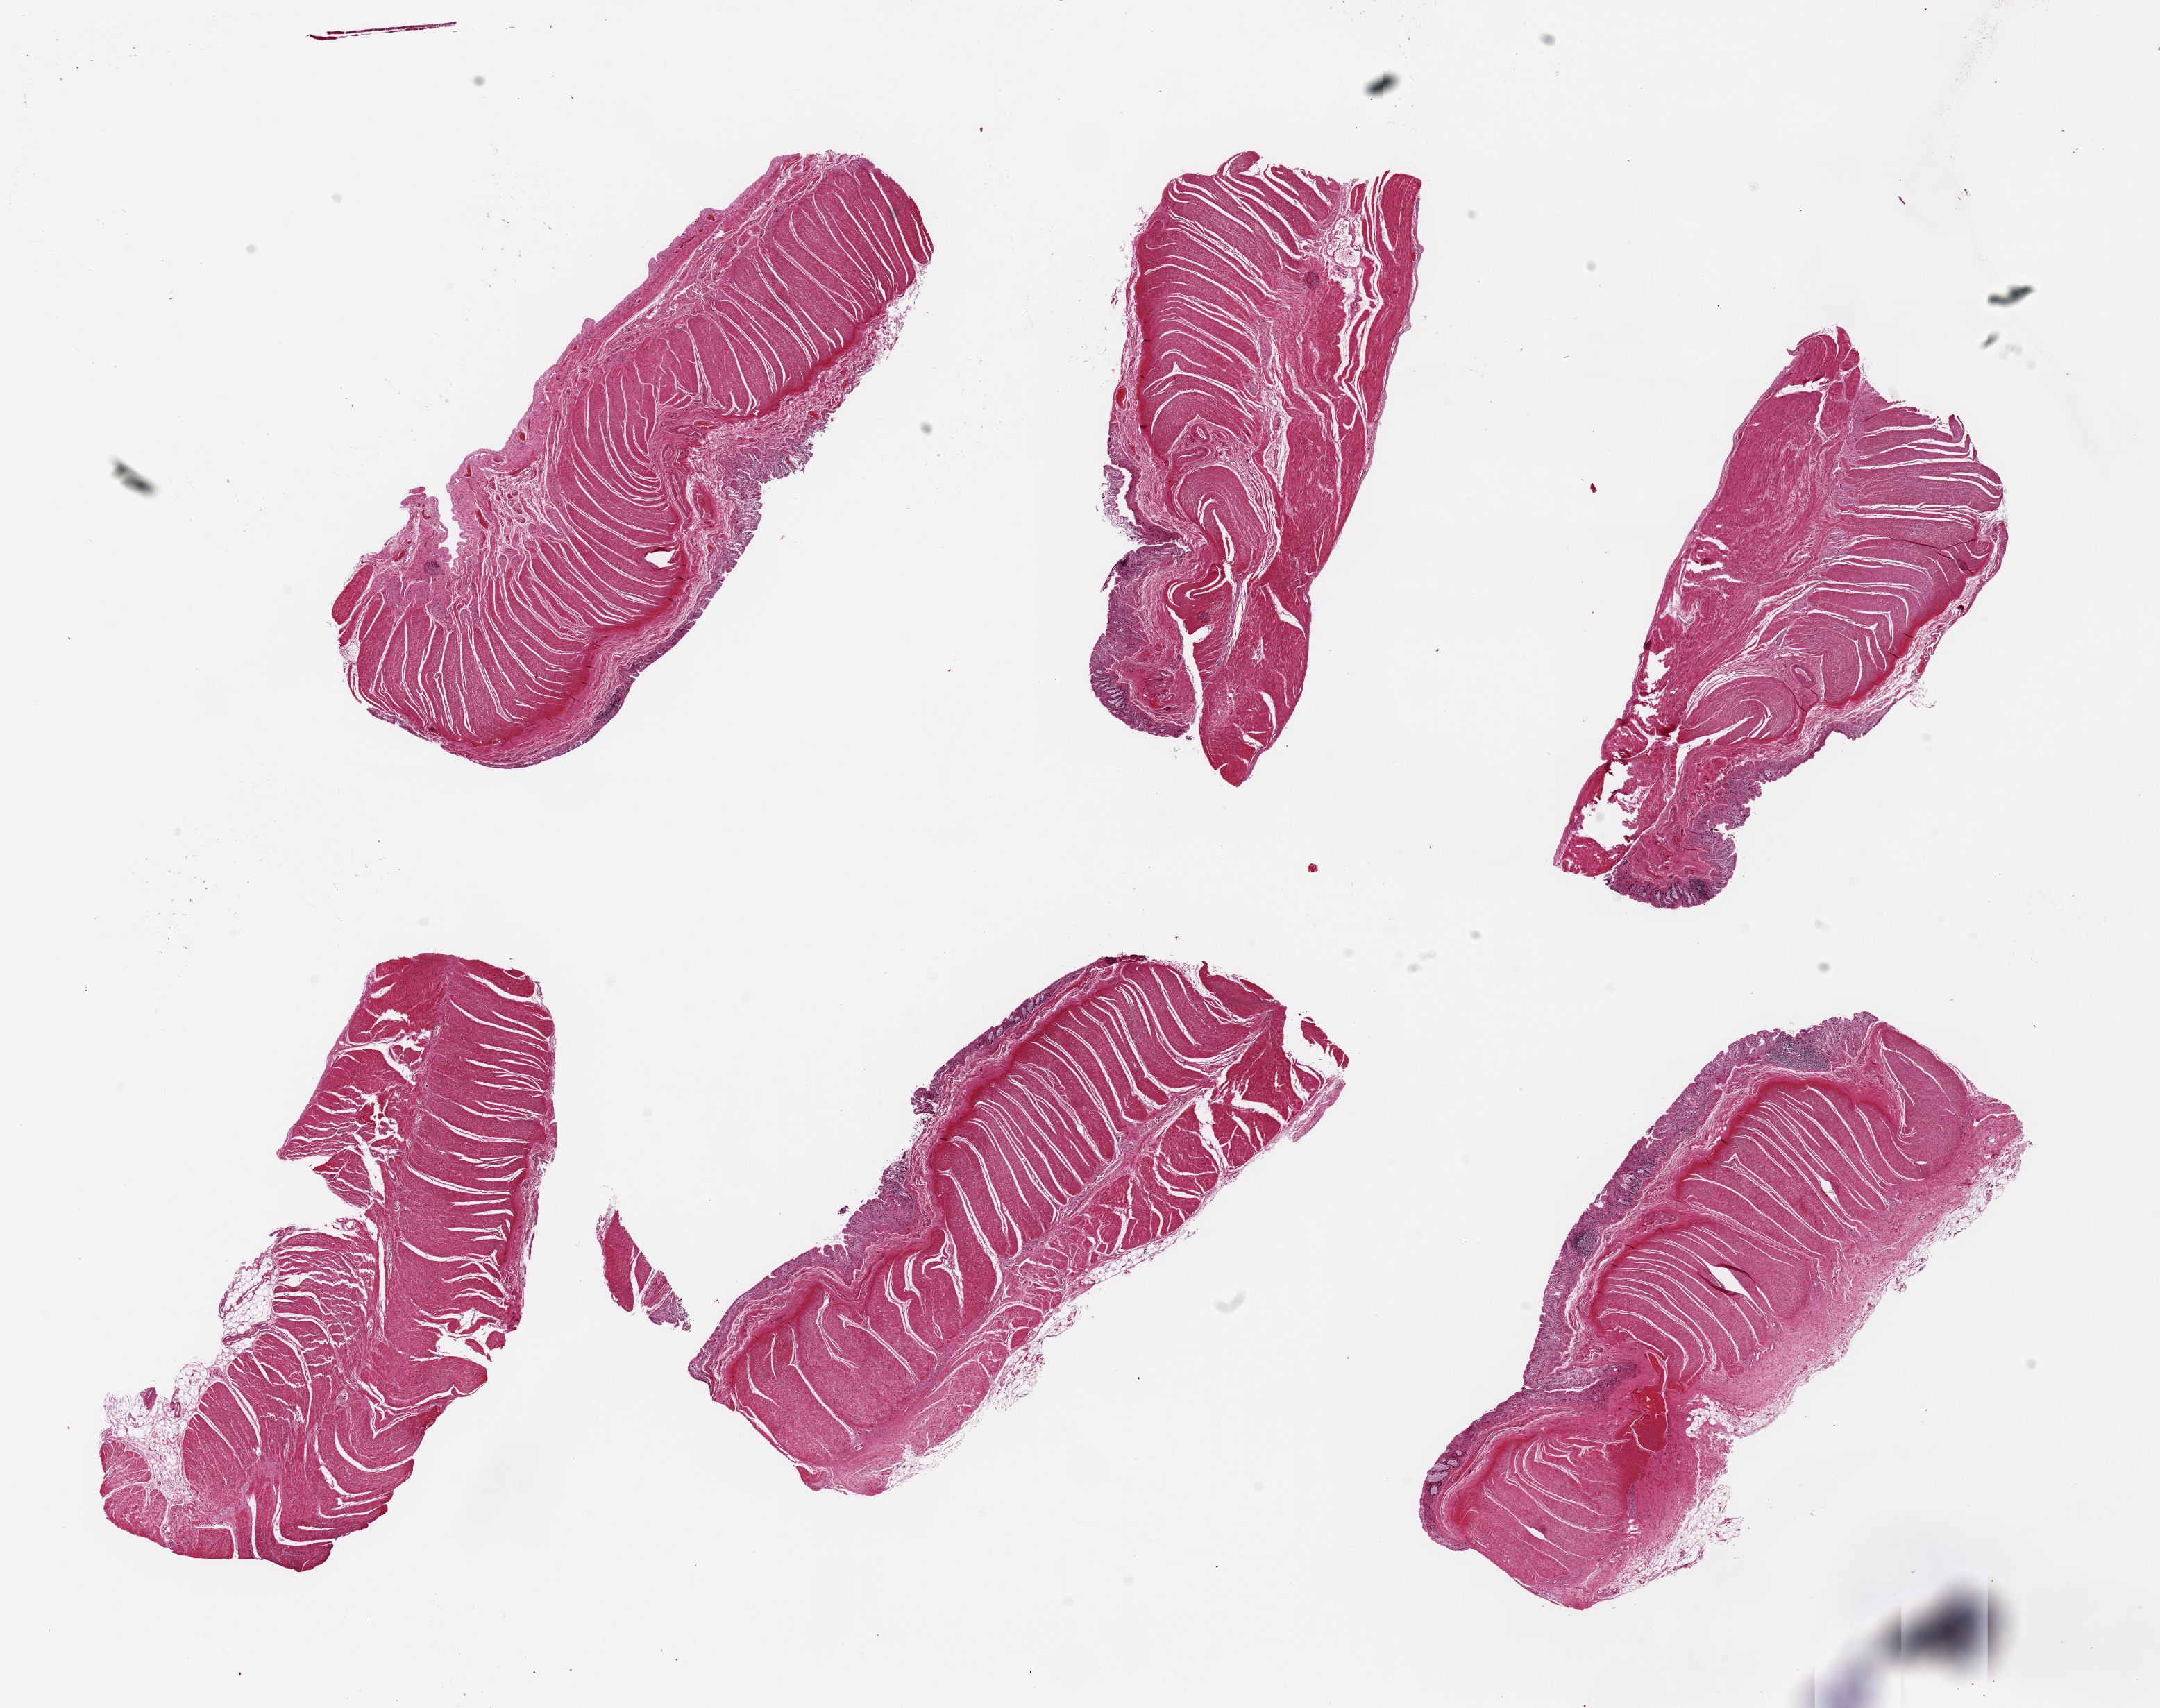
Hematoxylin and eosin (H&E) whole-slide image — shown as a low-resolution overview of the whole scanned area (about 24.6 x 19.5 mm). PAXgene-fixed paraffin-embedded (PFPE) section. Target tissue: sigmoid colon. Tissue donor sample. Donor: male.
• reviewer comment on this tissue sample: 6 pieces, up to 8x3.5mm; only 1 is free of mucosa, 5 have UNWANTED mucosa; musc=2, mucosa=3 (autolysis)